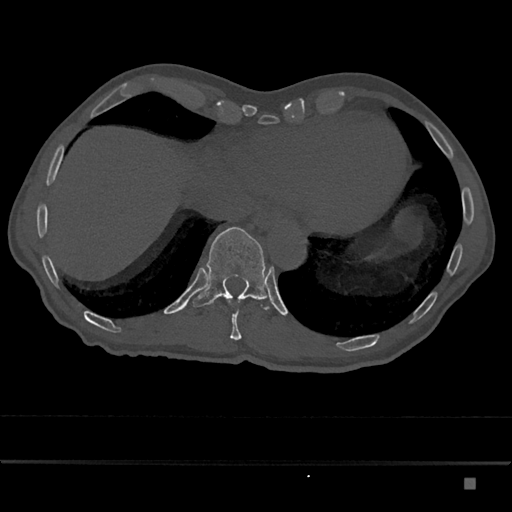
CT including the spine, one axial slice; position 700 of 797 along the scan axis; reconstruction kernel Br40s/3; bone window (W 1800 / L 400 HU); 0.5 mm slice thickness; 512 × 512 image matrix, field of view 390 × 390 mm. Patient: male, 72 years. From the clinical record (not read from this slice): primary cancer: prostate.
Outlined on this slice (semi-automatically segmented with operator editing):
- T10 vertebra: bounding box [x1, y1, x2, y2] px = [228, 298, 242, 340]
- T11 vertebra: [192, 227, 270, 310]